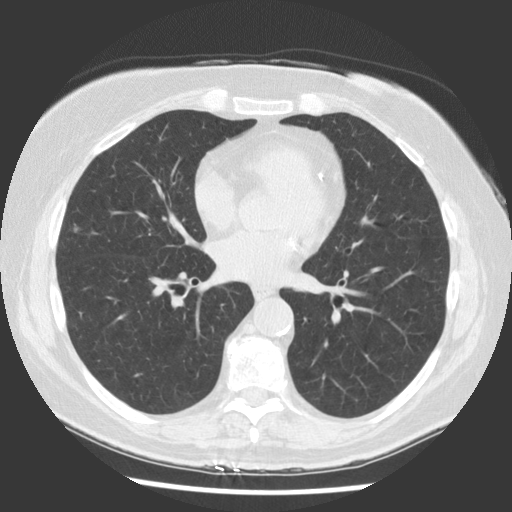
Low-dose screening chest CT, axial slice, baseline screening round, lung window (W 1500 / L -600 HU), 2.5 mm slice thickness, standard (soft-tissue) reconstruction kernel (STANDARD), slice 74 of 142 in the series, 512 × 512 image matrix, field of view 340 × 340 mm. Female participant, aged 66 years at enrolment.
Lesion marked by an expert reader, bounding box [x1, y1, x2, y2] px = [49, 208, 98, 249]. The screening reader recorded 2 non-calcified nodules or masses ≥4 mm on this exam (right middle lobe, right lower lobe); which of them this box marks is not recorded. Official screen result: positive, change unspecified: nodule(s) >= 4 mm or enlarging nodule(s), mass(es), or other non-specific abnormalities suspicious for lung cancer. Lung cancer was diagnosed 68 days after this screen: bronchiolo-alveolar carcinoma, mucinous, right middle lobe, well differentiated (G1), stage IA (AJCC 6th edition), 9 mm at pathology.